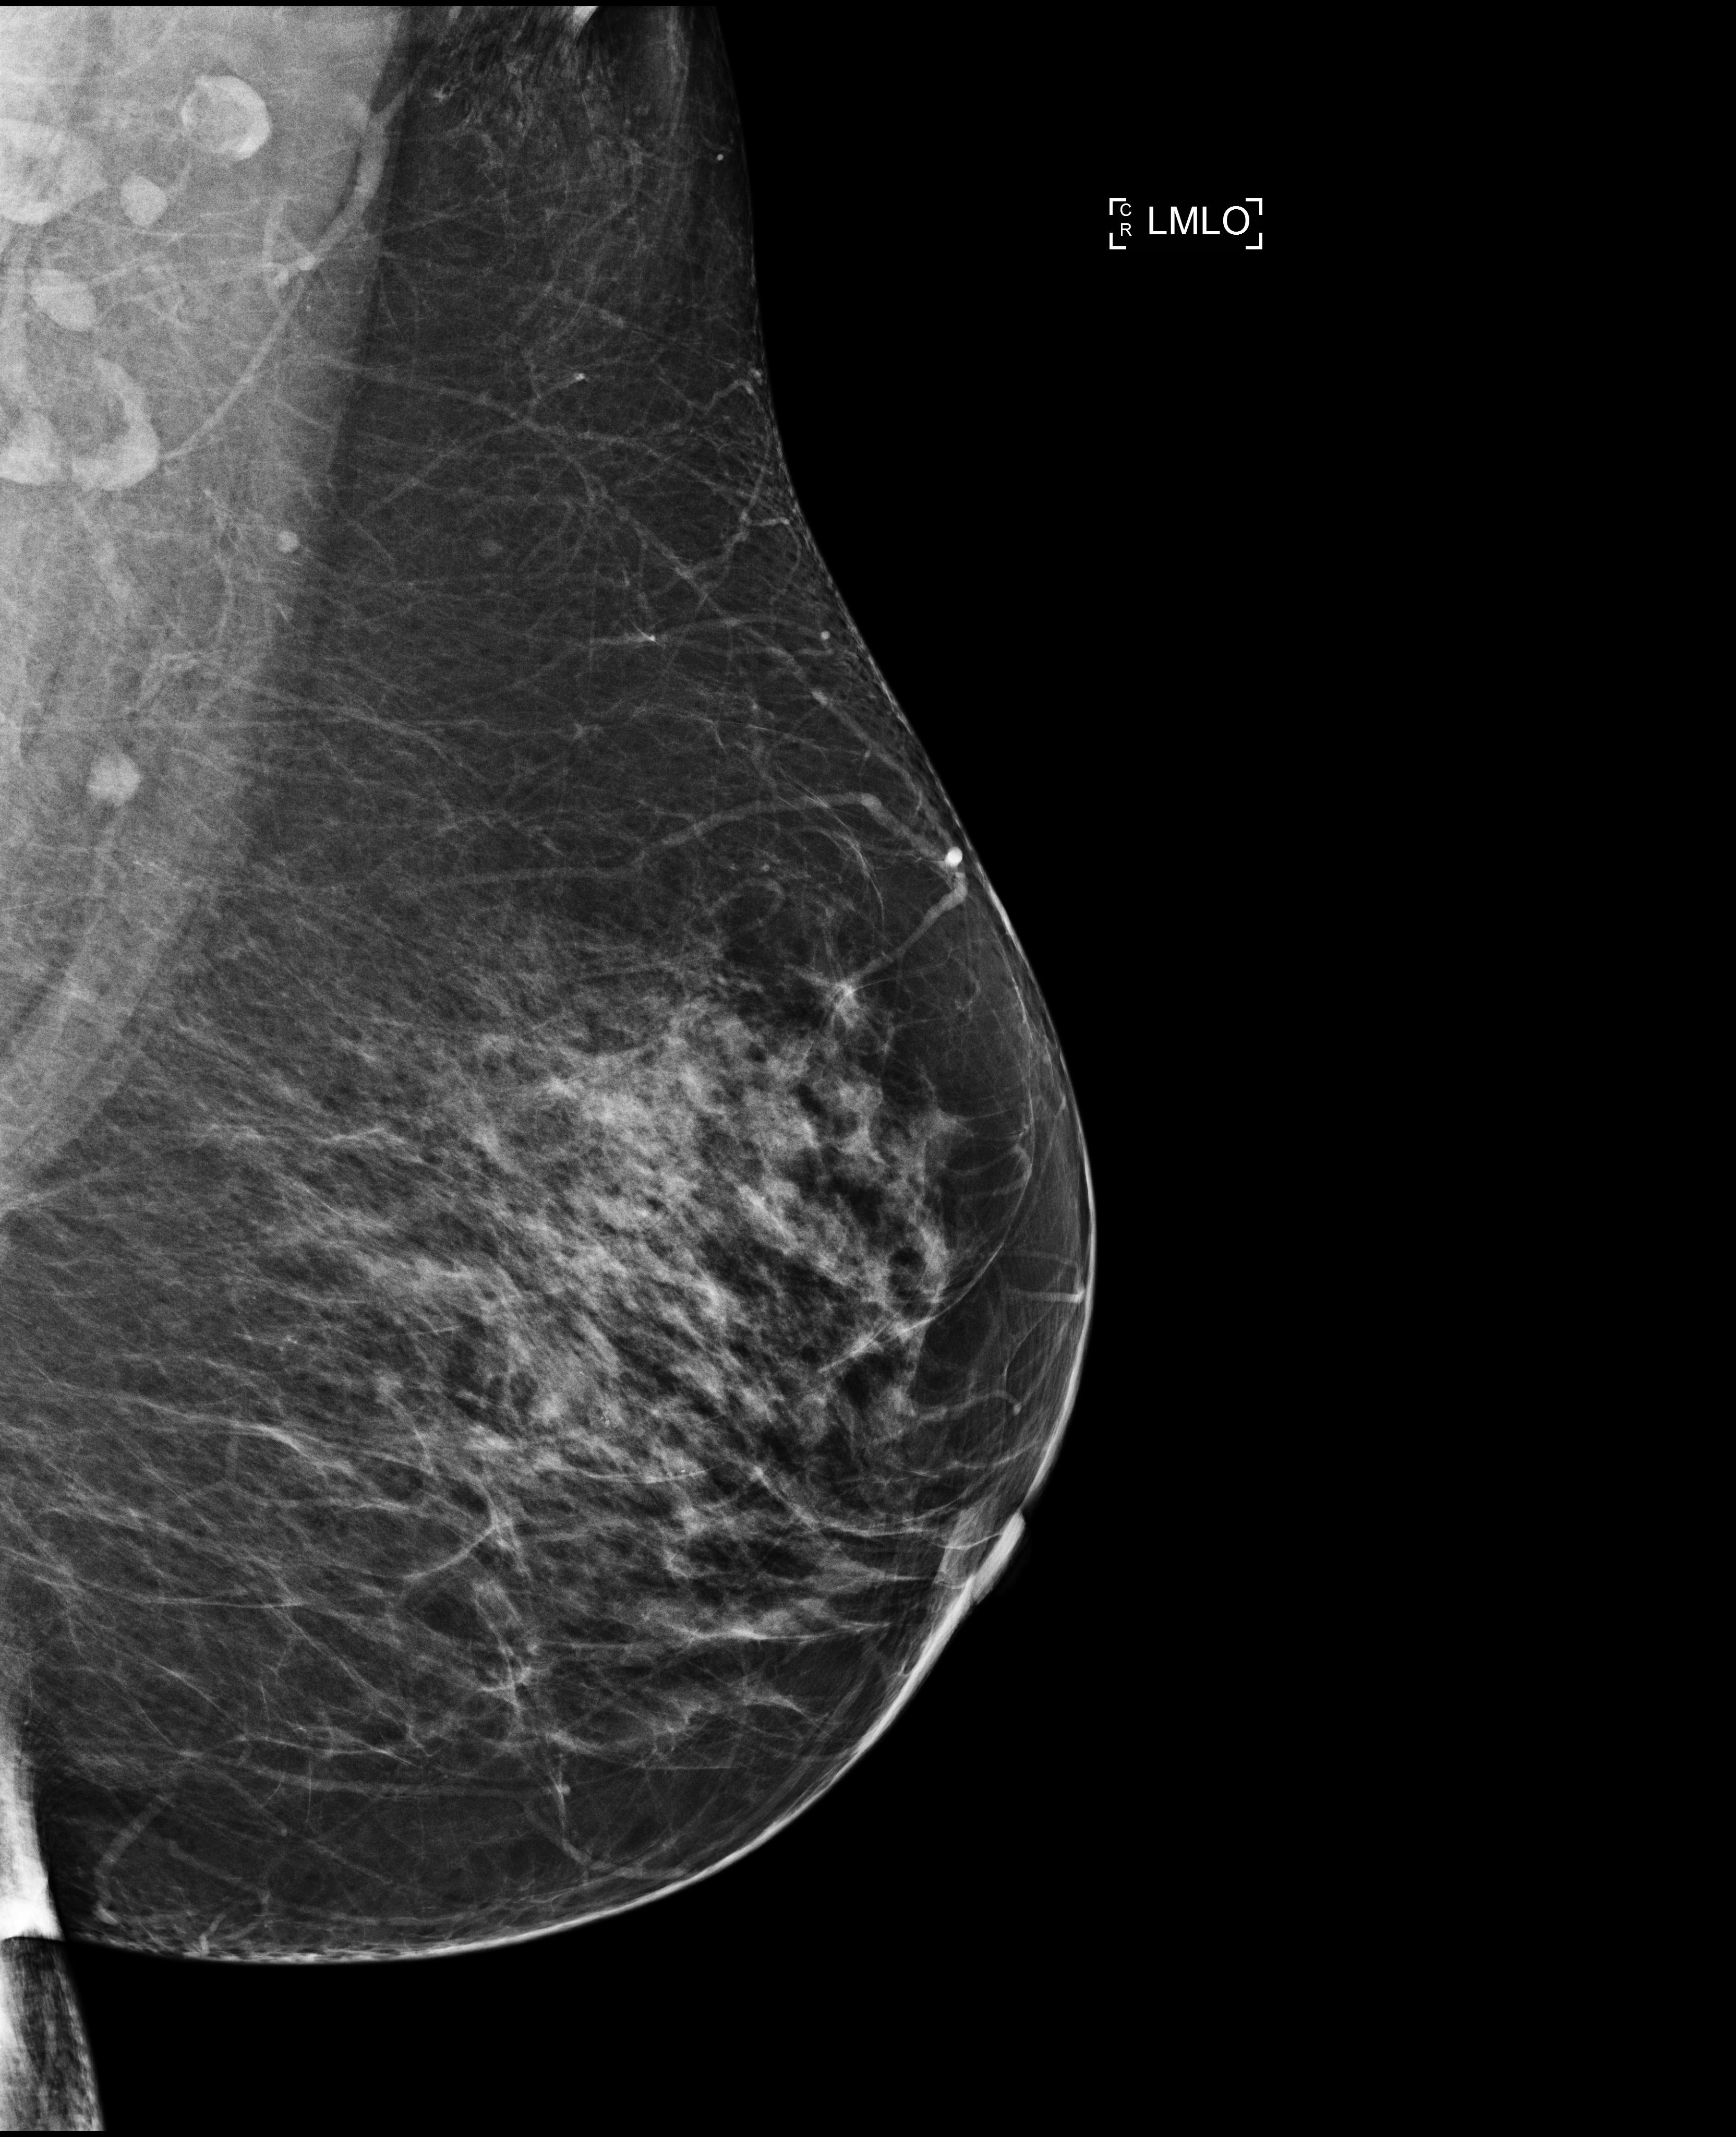
Screening examination; compressed breast thickness 60 mm. Patient: female, 58 years.
Image type: full-field digital mammogram. Breast: left. Projection: MLO view.